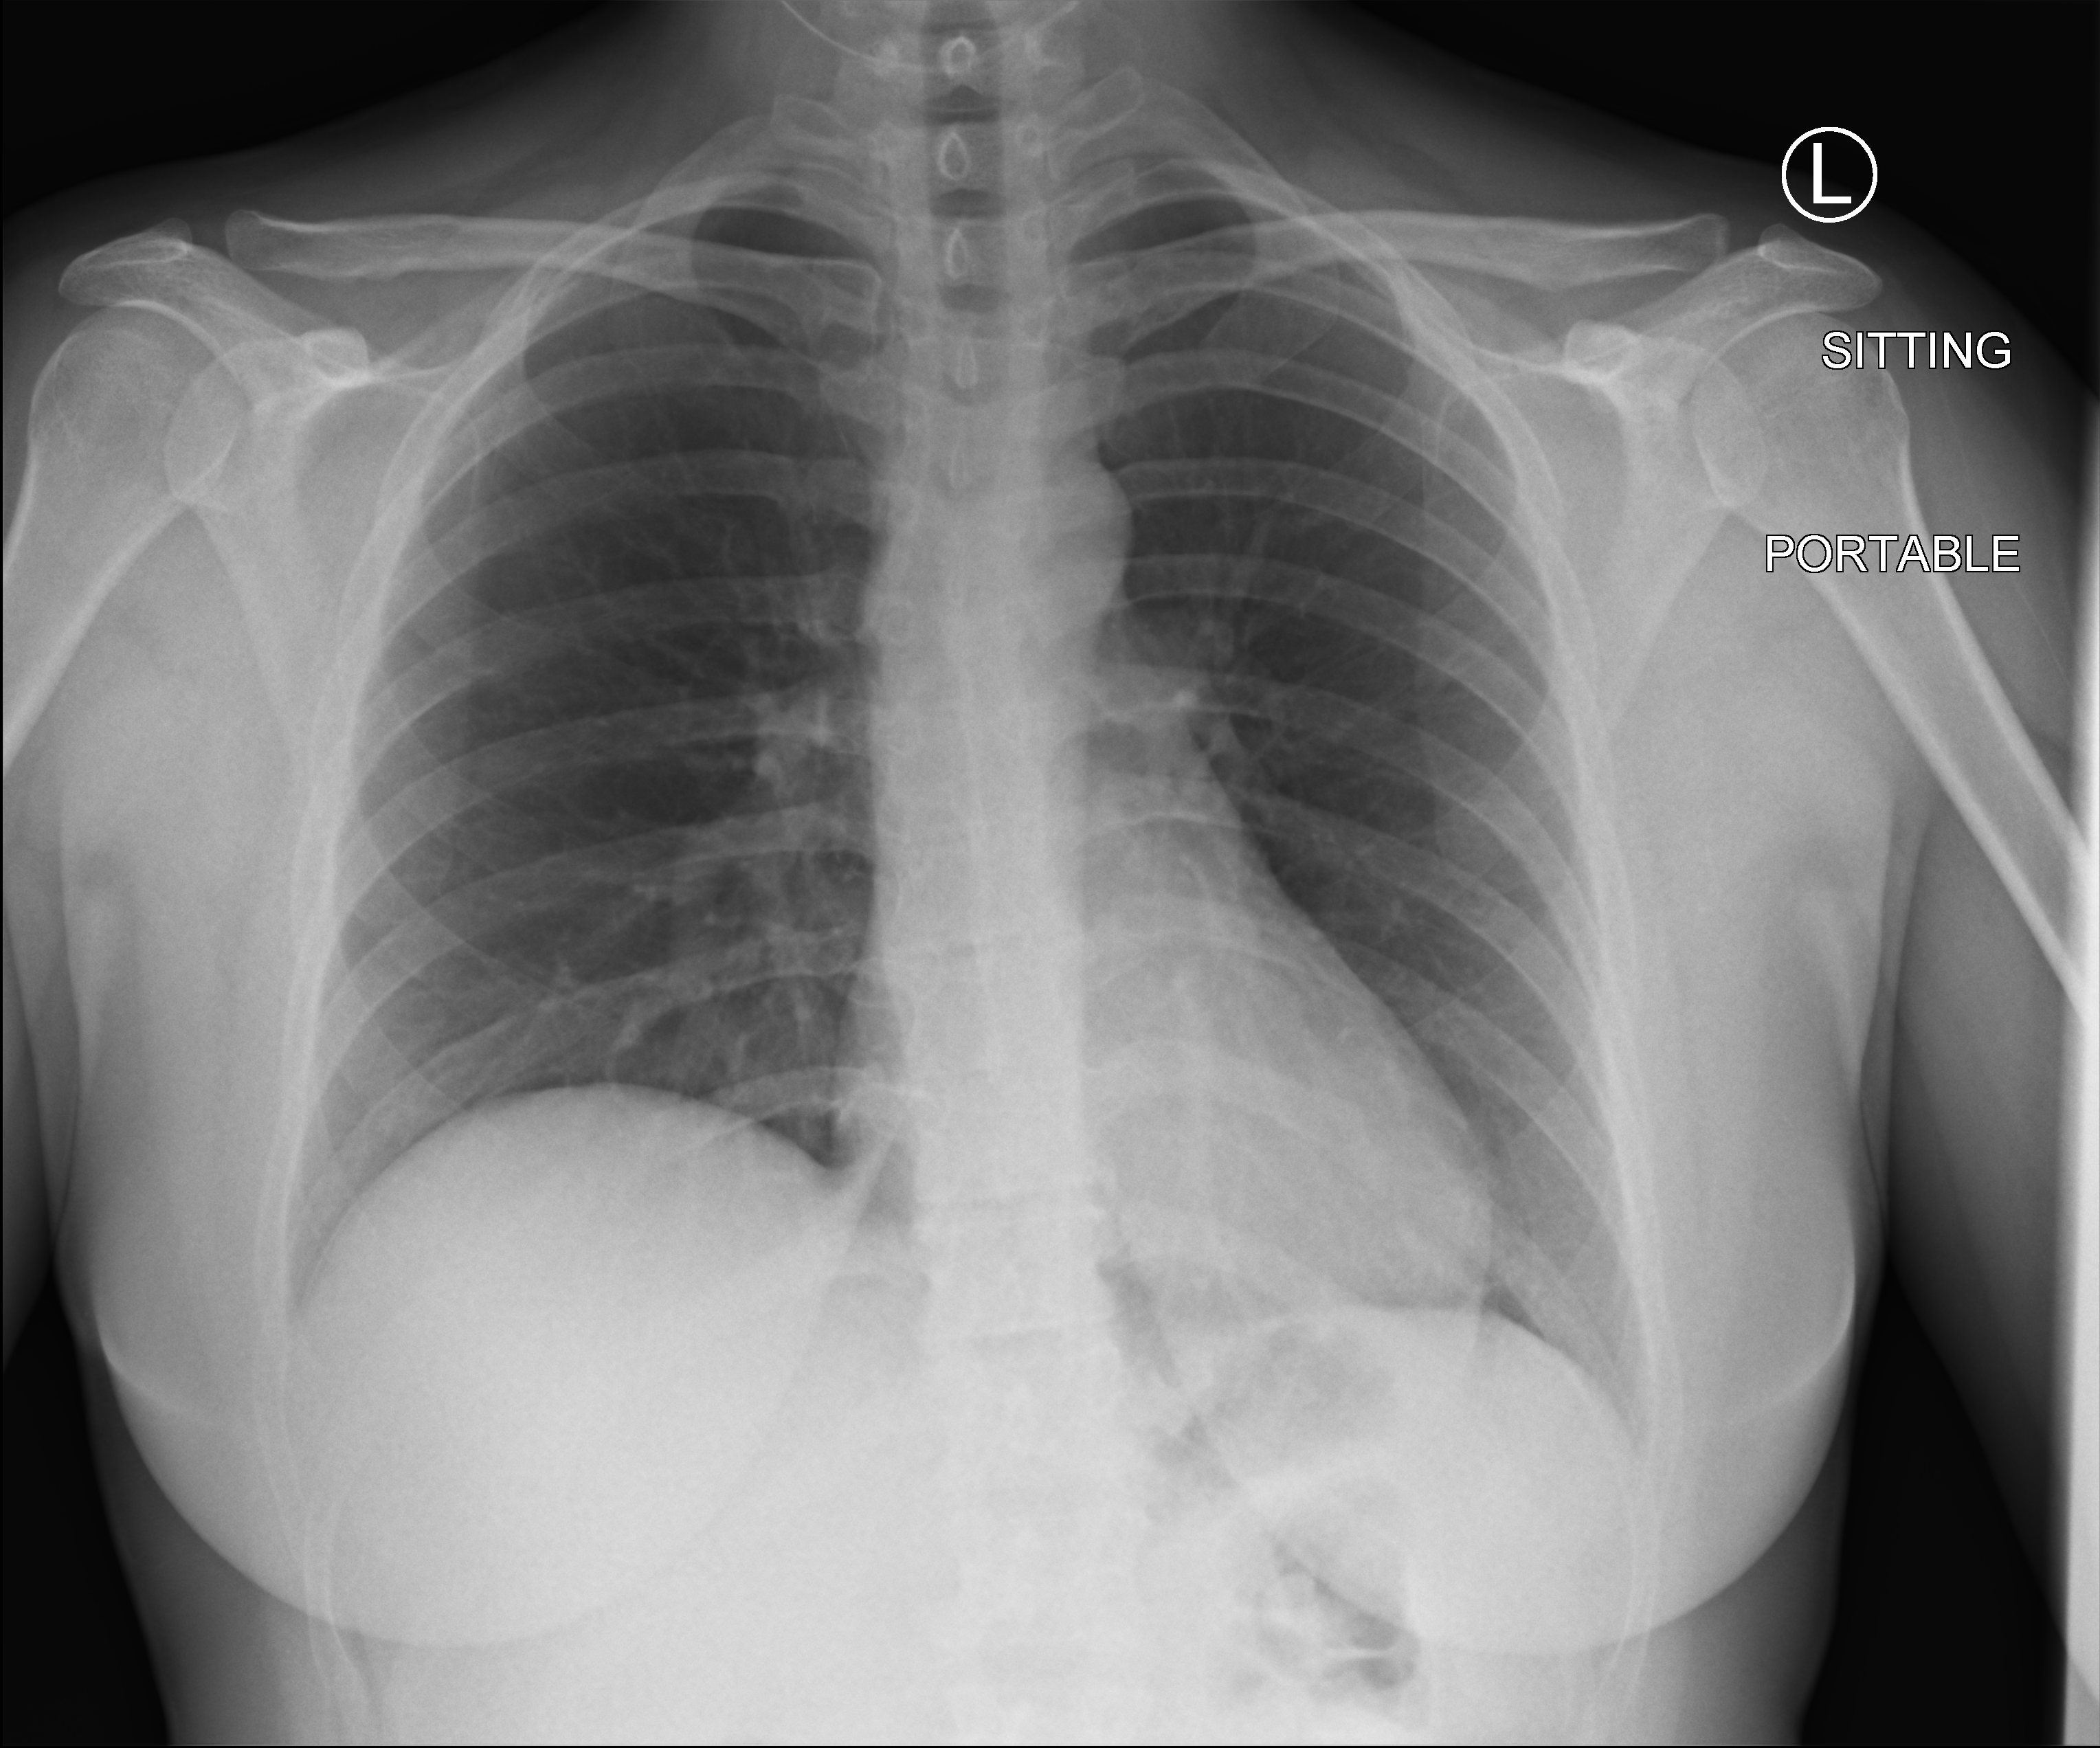
Portable chest radiograph; anteroposterior (AP) projection. Female patient hospitalised with COVID-19, age 18–59 years.
Admission-level facts for this patient (not findings on this image; timing relative to this image not recorded): admitted to intensive care during this hospital stay: no; mechanically ventilated during this hospital stay: no.